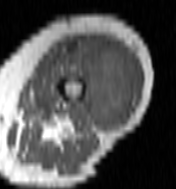
MRI of an extremity soft-tissue mass, one axial slice. Position 41 of 100 along the scan axis. MR volume resampled by the dataset authors to the PET/CT grid (not the native acquisition matrix). 176 × 189 image matrix. Female patient. Case-level facts recorded for this patient, not image findings: histological type: undifferentiated – high grade; grade: high; site of the primary tumour: left thigh.
Outlined on this slice (expert contour drawn on MRI and transferred to this co-registered scan by the dataset authors):
- gross tumour volume including surrounding oedema: bounding box [x1, y1, x2, y2] px = [60, 41, 136, 126]
- gross tumour volume (mass): [75, 41, 134, 126]